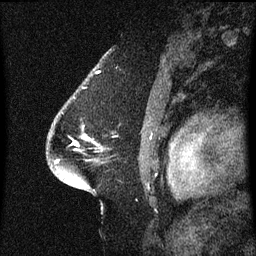
Breast MRI (dynamic contrast-enhanced), one sagittal slice; slice 45 of 60 in the series (ordered by position); dynamic contrast-enhanced series, image 2 of 3 at this slice position (ordered by acquisition); 1.5 T; TE 4.2 ms, TR 8.4 ms; 256 × 256 image matrix, field of view 200 × 200 mm. Female patient, age 54 years. Case-level facts recorded for this patient, not image findings: setting: breast cancer imaged before/during neoadjuvant chemotherapy; receptor status: HR-positive, HER2-negative.
Outlined on this slice (semi-automatically segmented with operator editing):
- analysis volume of interest (the breast-tissue region the enhancement analysis was run in; not a lesion): bounding box (x1, y1, x2, y2) in pixels: (52, 136, 103, 171)
- tumour enhancement mask (voxels above the 70 % enhancement threshold inside the analysis volume of interest): (85, 136, 90, 139)